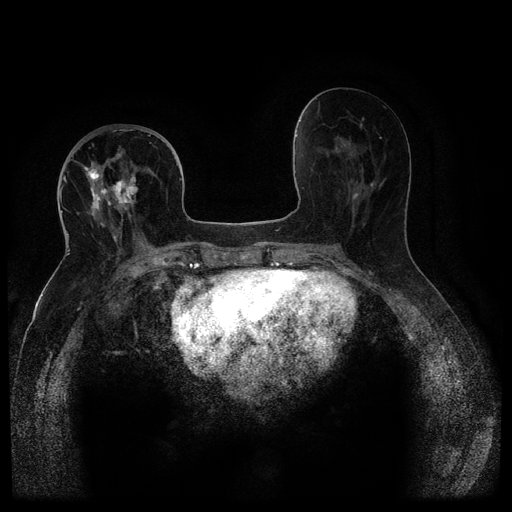
Breast MRI (dynamic contrast-enhanced, multi-phase), one axial slice. Slice 49 of 116 in the series (ordered by position). Dynamic contrast-enhanced series, time point 2 of 5 at this slice position (early post-contrast). 1.5 T. TE 2.6 ms, TR 5.4 ms. 512 × 512 image matrix, field of view 340 × 340 mm. Female patient, age 68 years.
Outlined on this slice (semi-automatic segmentation, software-assisted and operator-edited):
- breast lesion (labelled 'tumour' in the annotation; benign lesions carry a separate 'benign' label): bounding box [x1, y1, x2, y2] px = [110, 168, 139, 206]
- breast lesion (labelled 'tumour' in the annotation; benign lesions carry a separate 'benign' label): [85, 161, 108, 228]